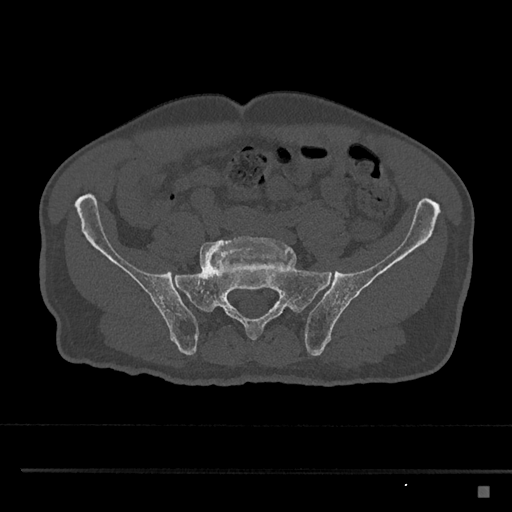
CT including the spine, one axial slice; slice 541 of 797 in the series (ordered by position); reconstruction kernel Br40s/3; bone window (W 1800 / L 400 HU); 0.5 mm slice thickness; 512 × 512 image matrix, field of view 391 × 391 mm. Male patient, age 59 years. From the clinical record (not read from this slice): primary cancer: prostate.
Annotated regions visible in this slice (semi-automatic segmentation, software-assisted and operator-edited):
- L5 vertebra: box from (x=199, y=235) to (x=292, y=272) px